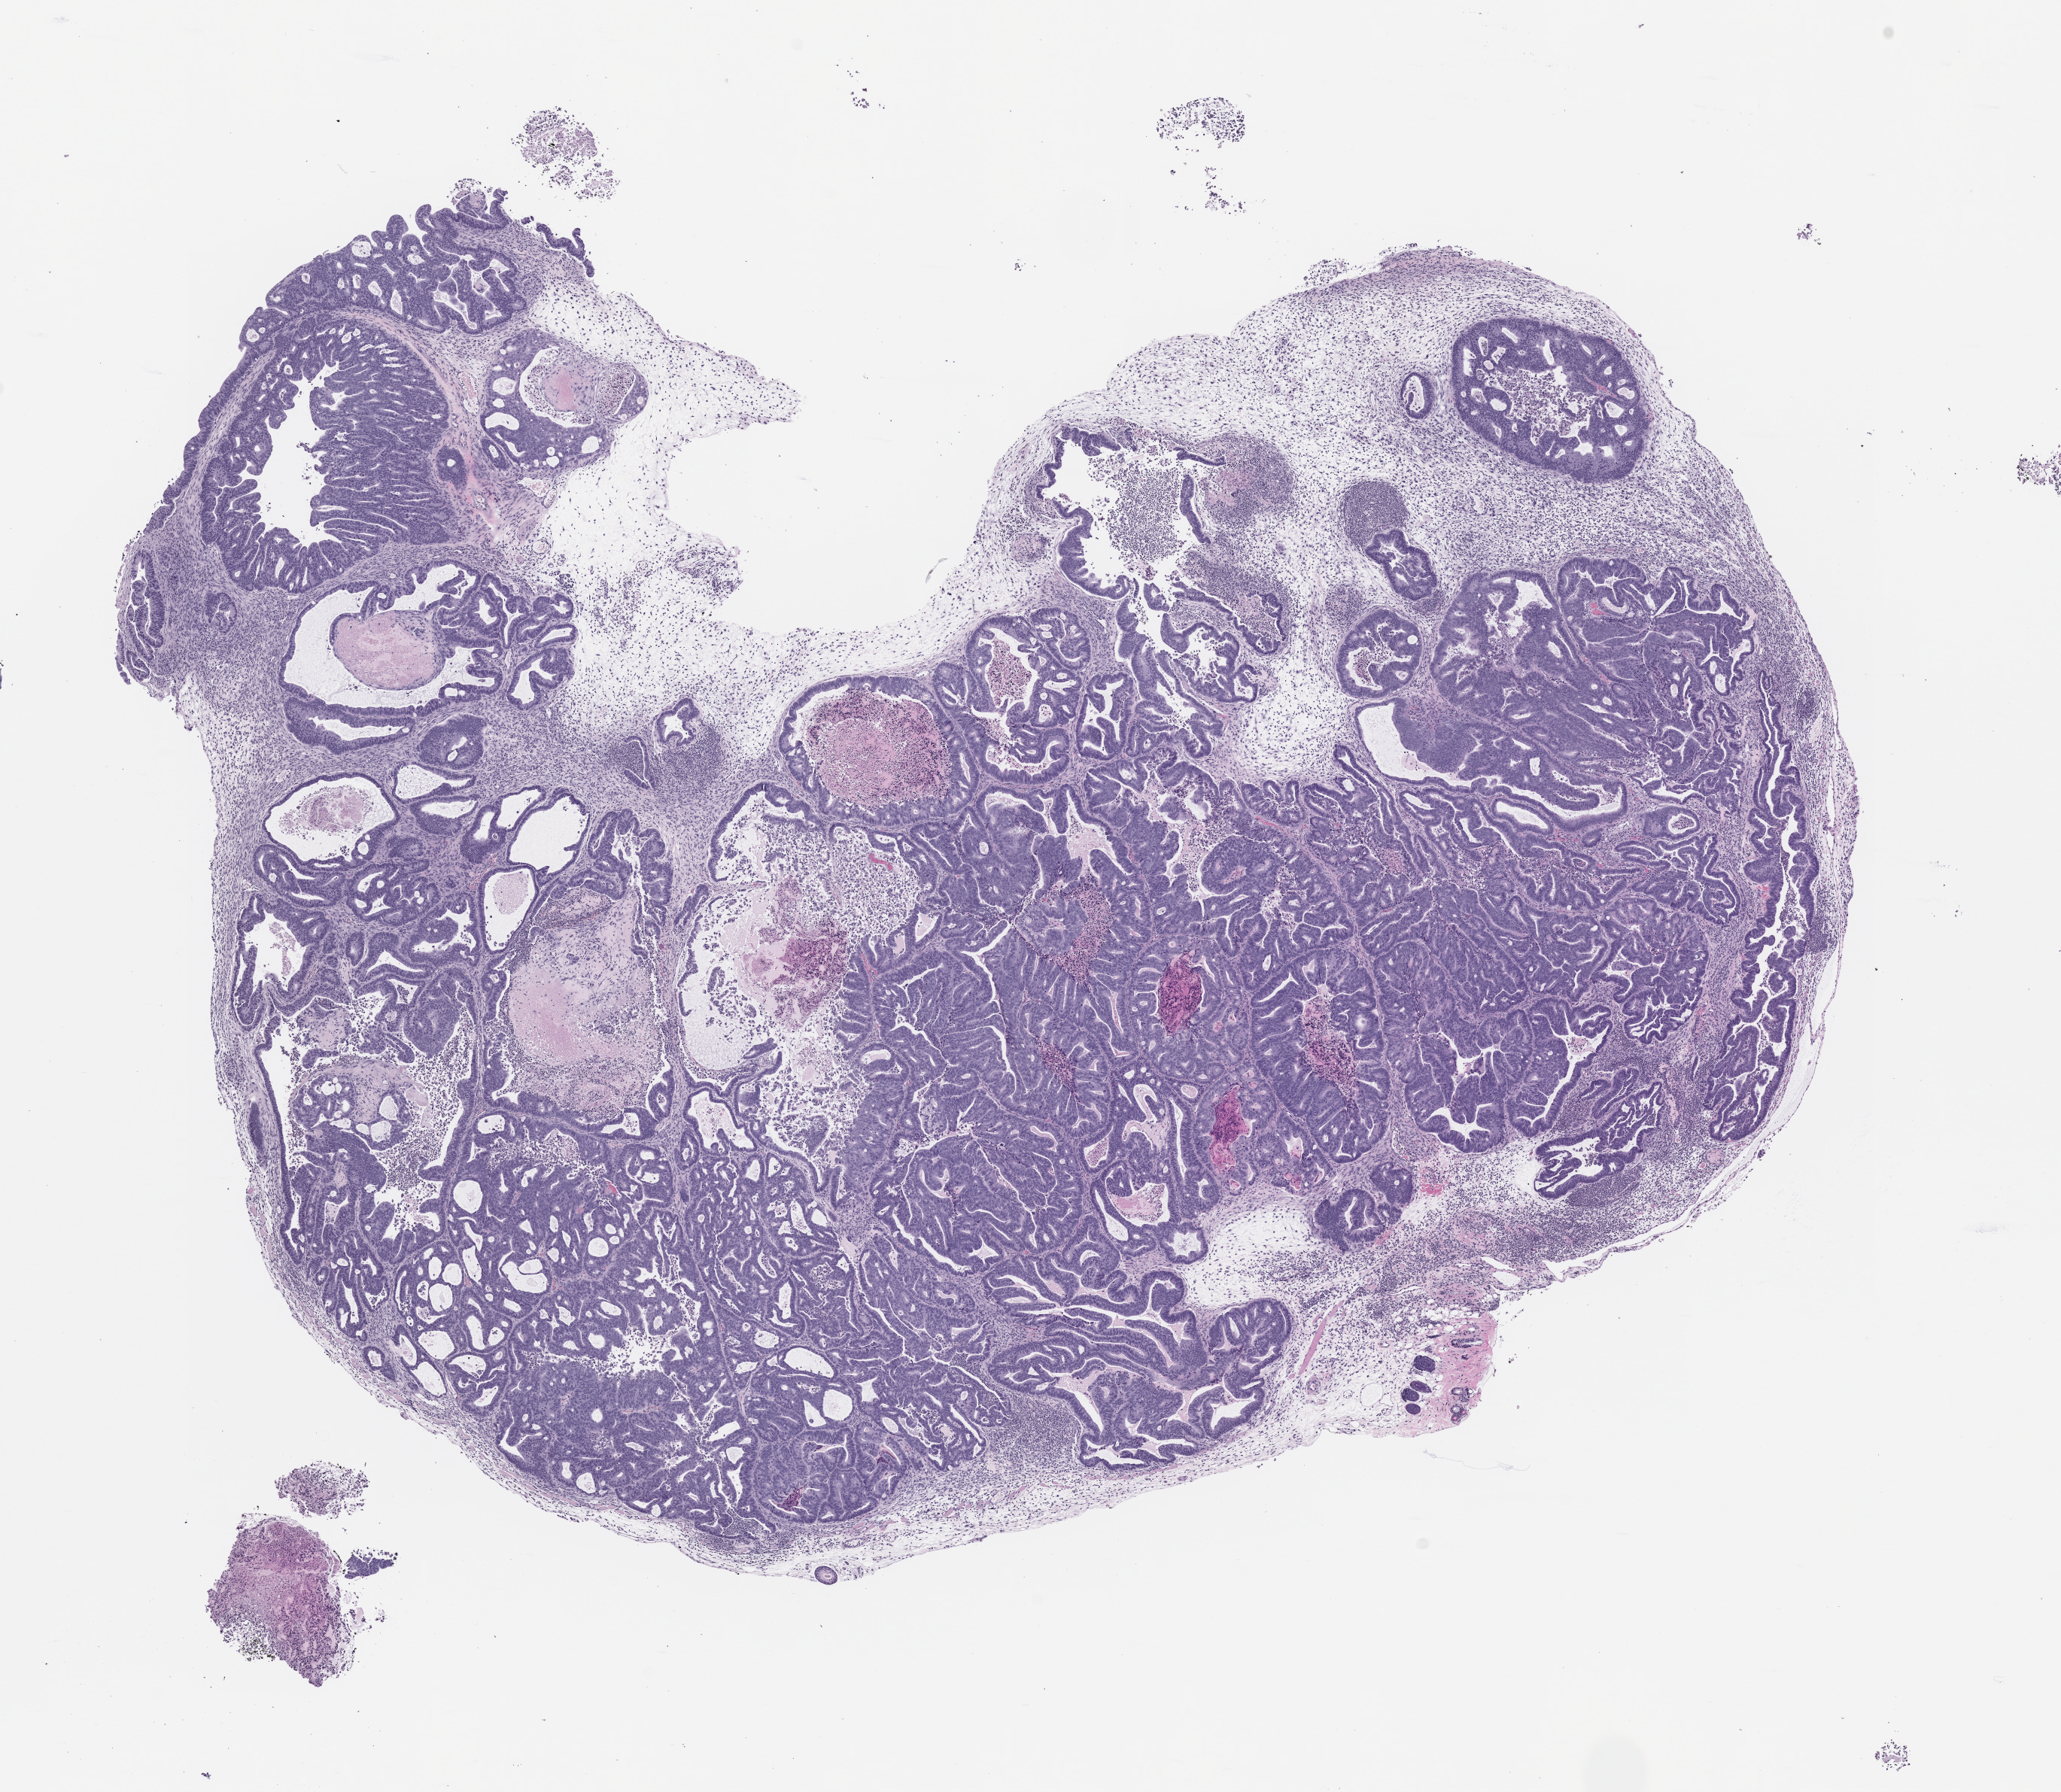
Hematoxylin and eosin (H&E) whole-slide image of a patient-derived xenograft (PDX) tumor grown in a mouse, passage 2 — shown as a low-resolution overview of the whole scanned area (about 11.0 x 9.6 mm); formalin-fixed, paraffin-embedded (FFPE) tissue; originating tumor site category: colon.
* originating patient diagnosis: Colon Adenocarcinoma